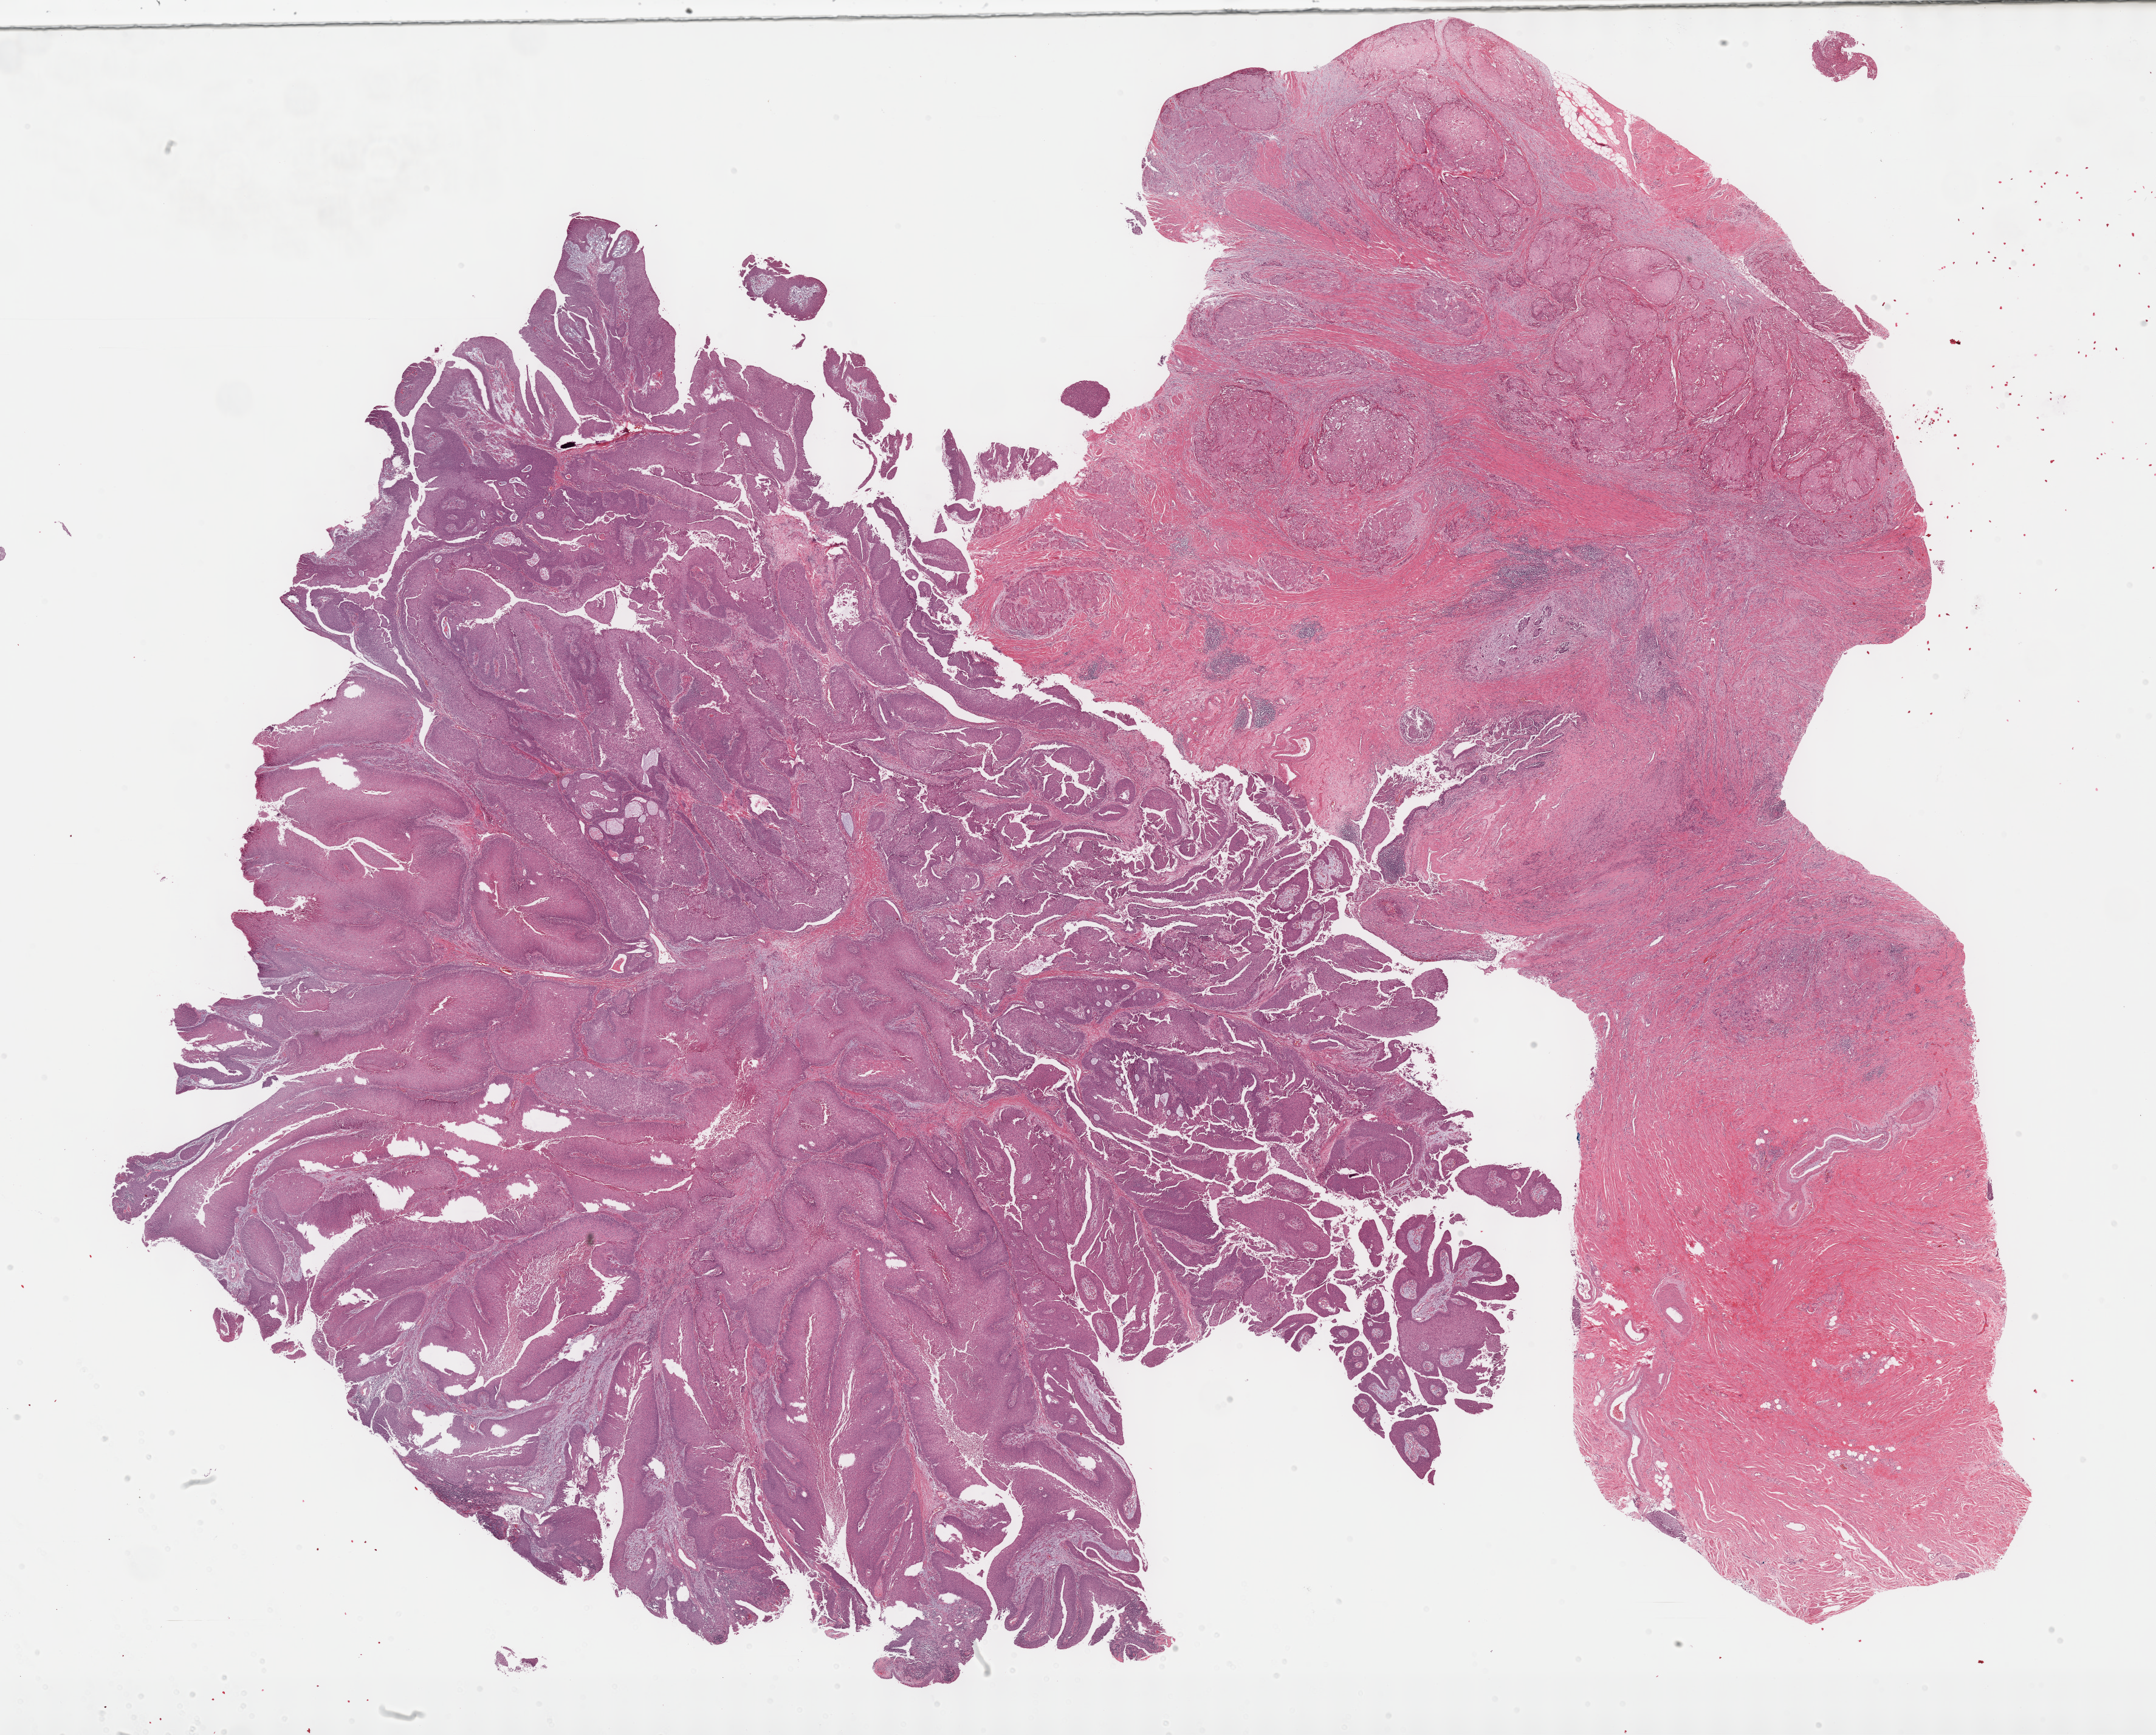
Whole-slide histology image, Hematoxylin and eosin (H&E) stained — low-resolution overview of the scanned area, about 28.7 x 23.1 mm; formalin-fixed paraffin-embedded (FFPE) diagnostic section; sample: primary tumour, bladder. Patient: female, age at initial diagnosis 57 years. Histologic grade: high grade.
- pathologic diagnosis: Papillary transitional cell carcinoma
- lymph nodes positive (case pathology): 32 of 61 examined
- TNM: T2b N2 MX
- AJCC pathologic stage: IV